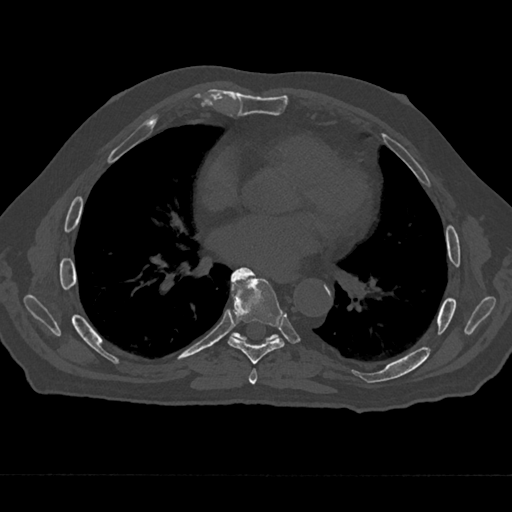
CT including the spine, one axial slice; position 358 of 797 along the scan axis; 120 kVp; bone window (W 1800 / L 400 HU); 0.5 mm slice thickness; 512 × 512 image matrix, field of view 377 × 377 mm. Patient: male, 75 years. From the clinical record (not read from this slice): primary cancer: renal; vertebrae with lytic lesions (as recorded): T4.
Structures marked on this image (semi-automatically segmented with operator editing):
- T6 vertebra: bounding box (x1, y1, x2, y2) in pixels: (249, 369, 258, 385)
- T7 vertebra: (228, 267, 285, 364)
- T8 vertebra: (231, 332, 279, 342)